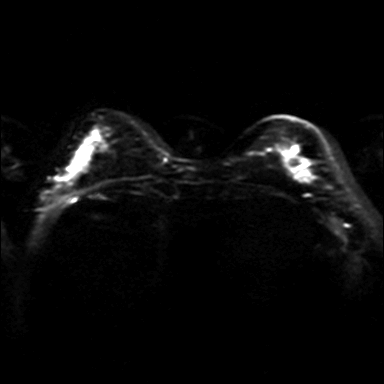
Breast MRI, one axial slice; slice 9 of 36 in the series (ordered by position); diffusion-weighted series; image 2 of 4 stored at this slice position (different b-values; order by instance number); 3 T; 384 × 384 image matrix, field of view 320 × 320 mm. Female patient.
Structures marked on this image (manually delineated by an expert):
- tumour on diffusion-weighted imaging: bounding box <297,170,312,181> (left, top, right, bottom; pixels)